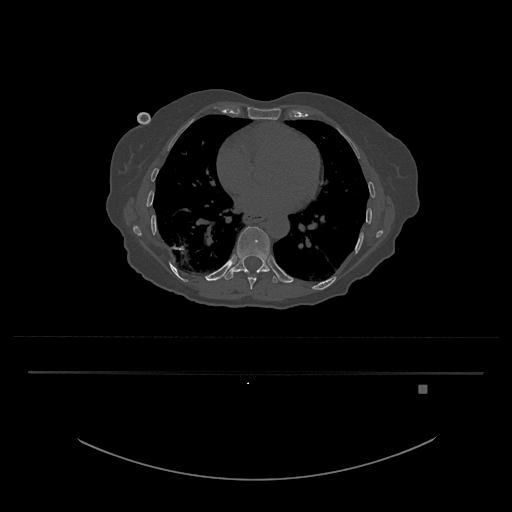
CT including the spine, one axial slice. Position 732 of 797 along the scan axis. Reconstruction kernel Br40s/3. Bone window (W 1800 / L 400 HU). 0.5 mm slice thickness. 512 × 512 image matrix, field of view 500 × 500 mm. Female patient, age 57 years. Case-level facts recorded for this patient, not image findings: primary cancer: cervical.
Structures marked on this image (semi-automatic segmentation, software-assisted and operator-edited):
- T10 vertebra: bounding box [x1, y1, x2, y2] px = [223, 227, 282, 283]
- T9 vertebra: [248, 277, 256, 289]